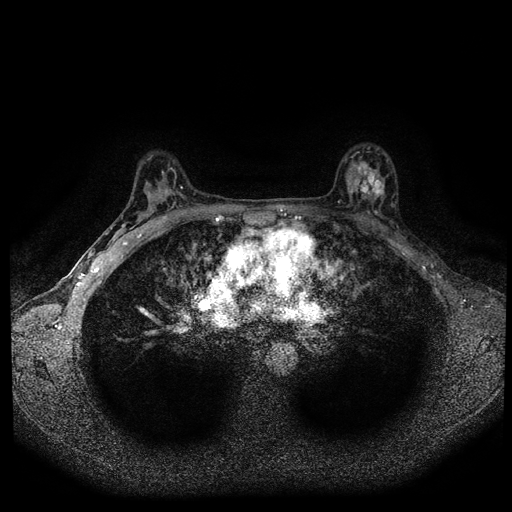
Breast MRI (dynamic contrast-enhanced, multi-phase), one axial slice. Slice 60 of 108 in the series (ordered by position). Dynamic contrast-enhanced series, time point 2 of 5 at this slice position (early post-contrast). 1.5 T. TE 2.7 ms, TR 5.5 ms. 2 mm slice thickness. 512 × 512 image matrix, field of view 320 × 320 mm. Female patient, age 36 years.
Structures marked on this image (semi-automatic segmentation, software-assisted and operator-edited):
- breast lesion (labelled 'tumour' in the annotation; benign lesions carry a separate 'benign' label): bounding box (x1, y1, x2, y2) in pixels: (339, 156, 385, 205)